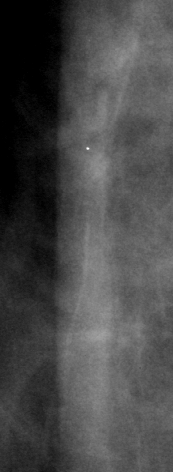
Cropped region of a digitized screen-film mammogram centred on a radiologist-marked abnormality, right breast, CC view.
Marked abnormality: mass, shape architectural distortion; BI-RADS assessment category 2; pathology result (as recorded, not read from the image): benign.